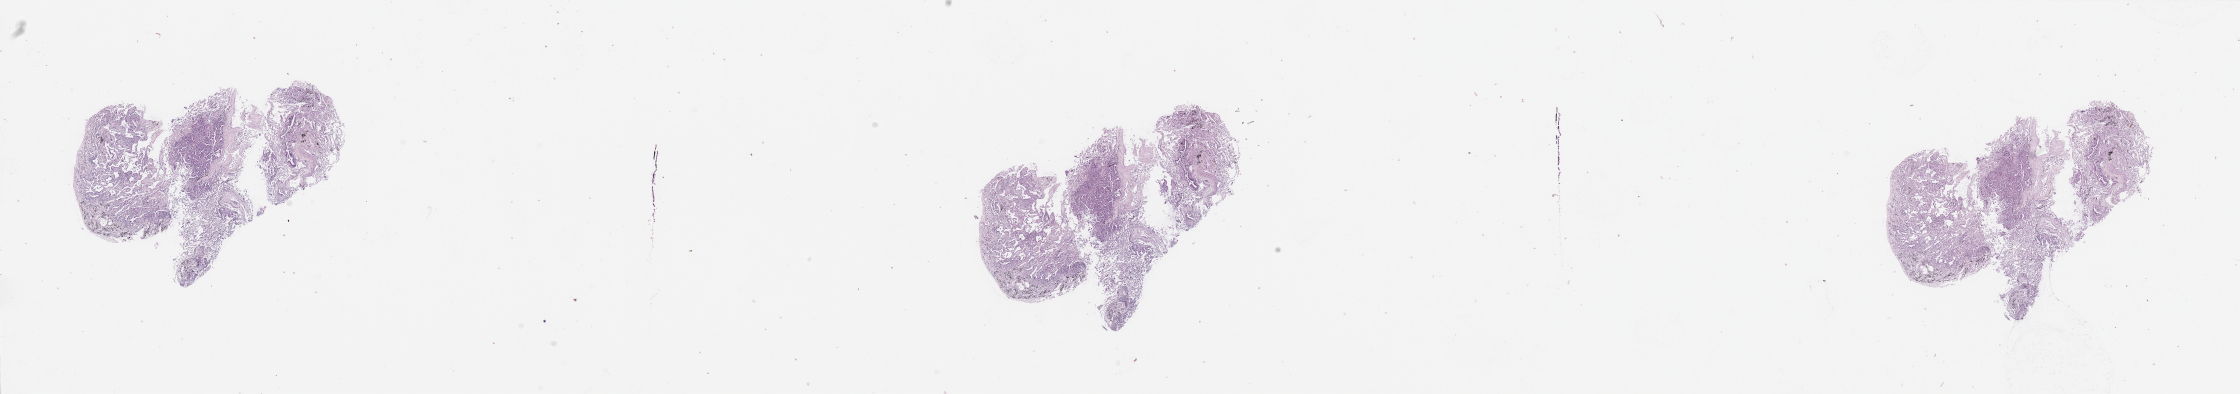
Digitized H&E tissue section (whole slide) — low-resolution overview of the scanned area, about 35.4 x 6.2 mm (from a 20x scan). Normal (non-tumour) tissue sample, lung. 77-year-old male patient.
This section: normal (non-tumour) tissue from the same patient. Patient diagnosis: Adenocarcinoma, NOS.